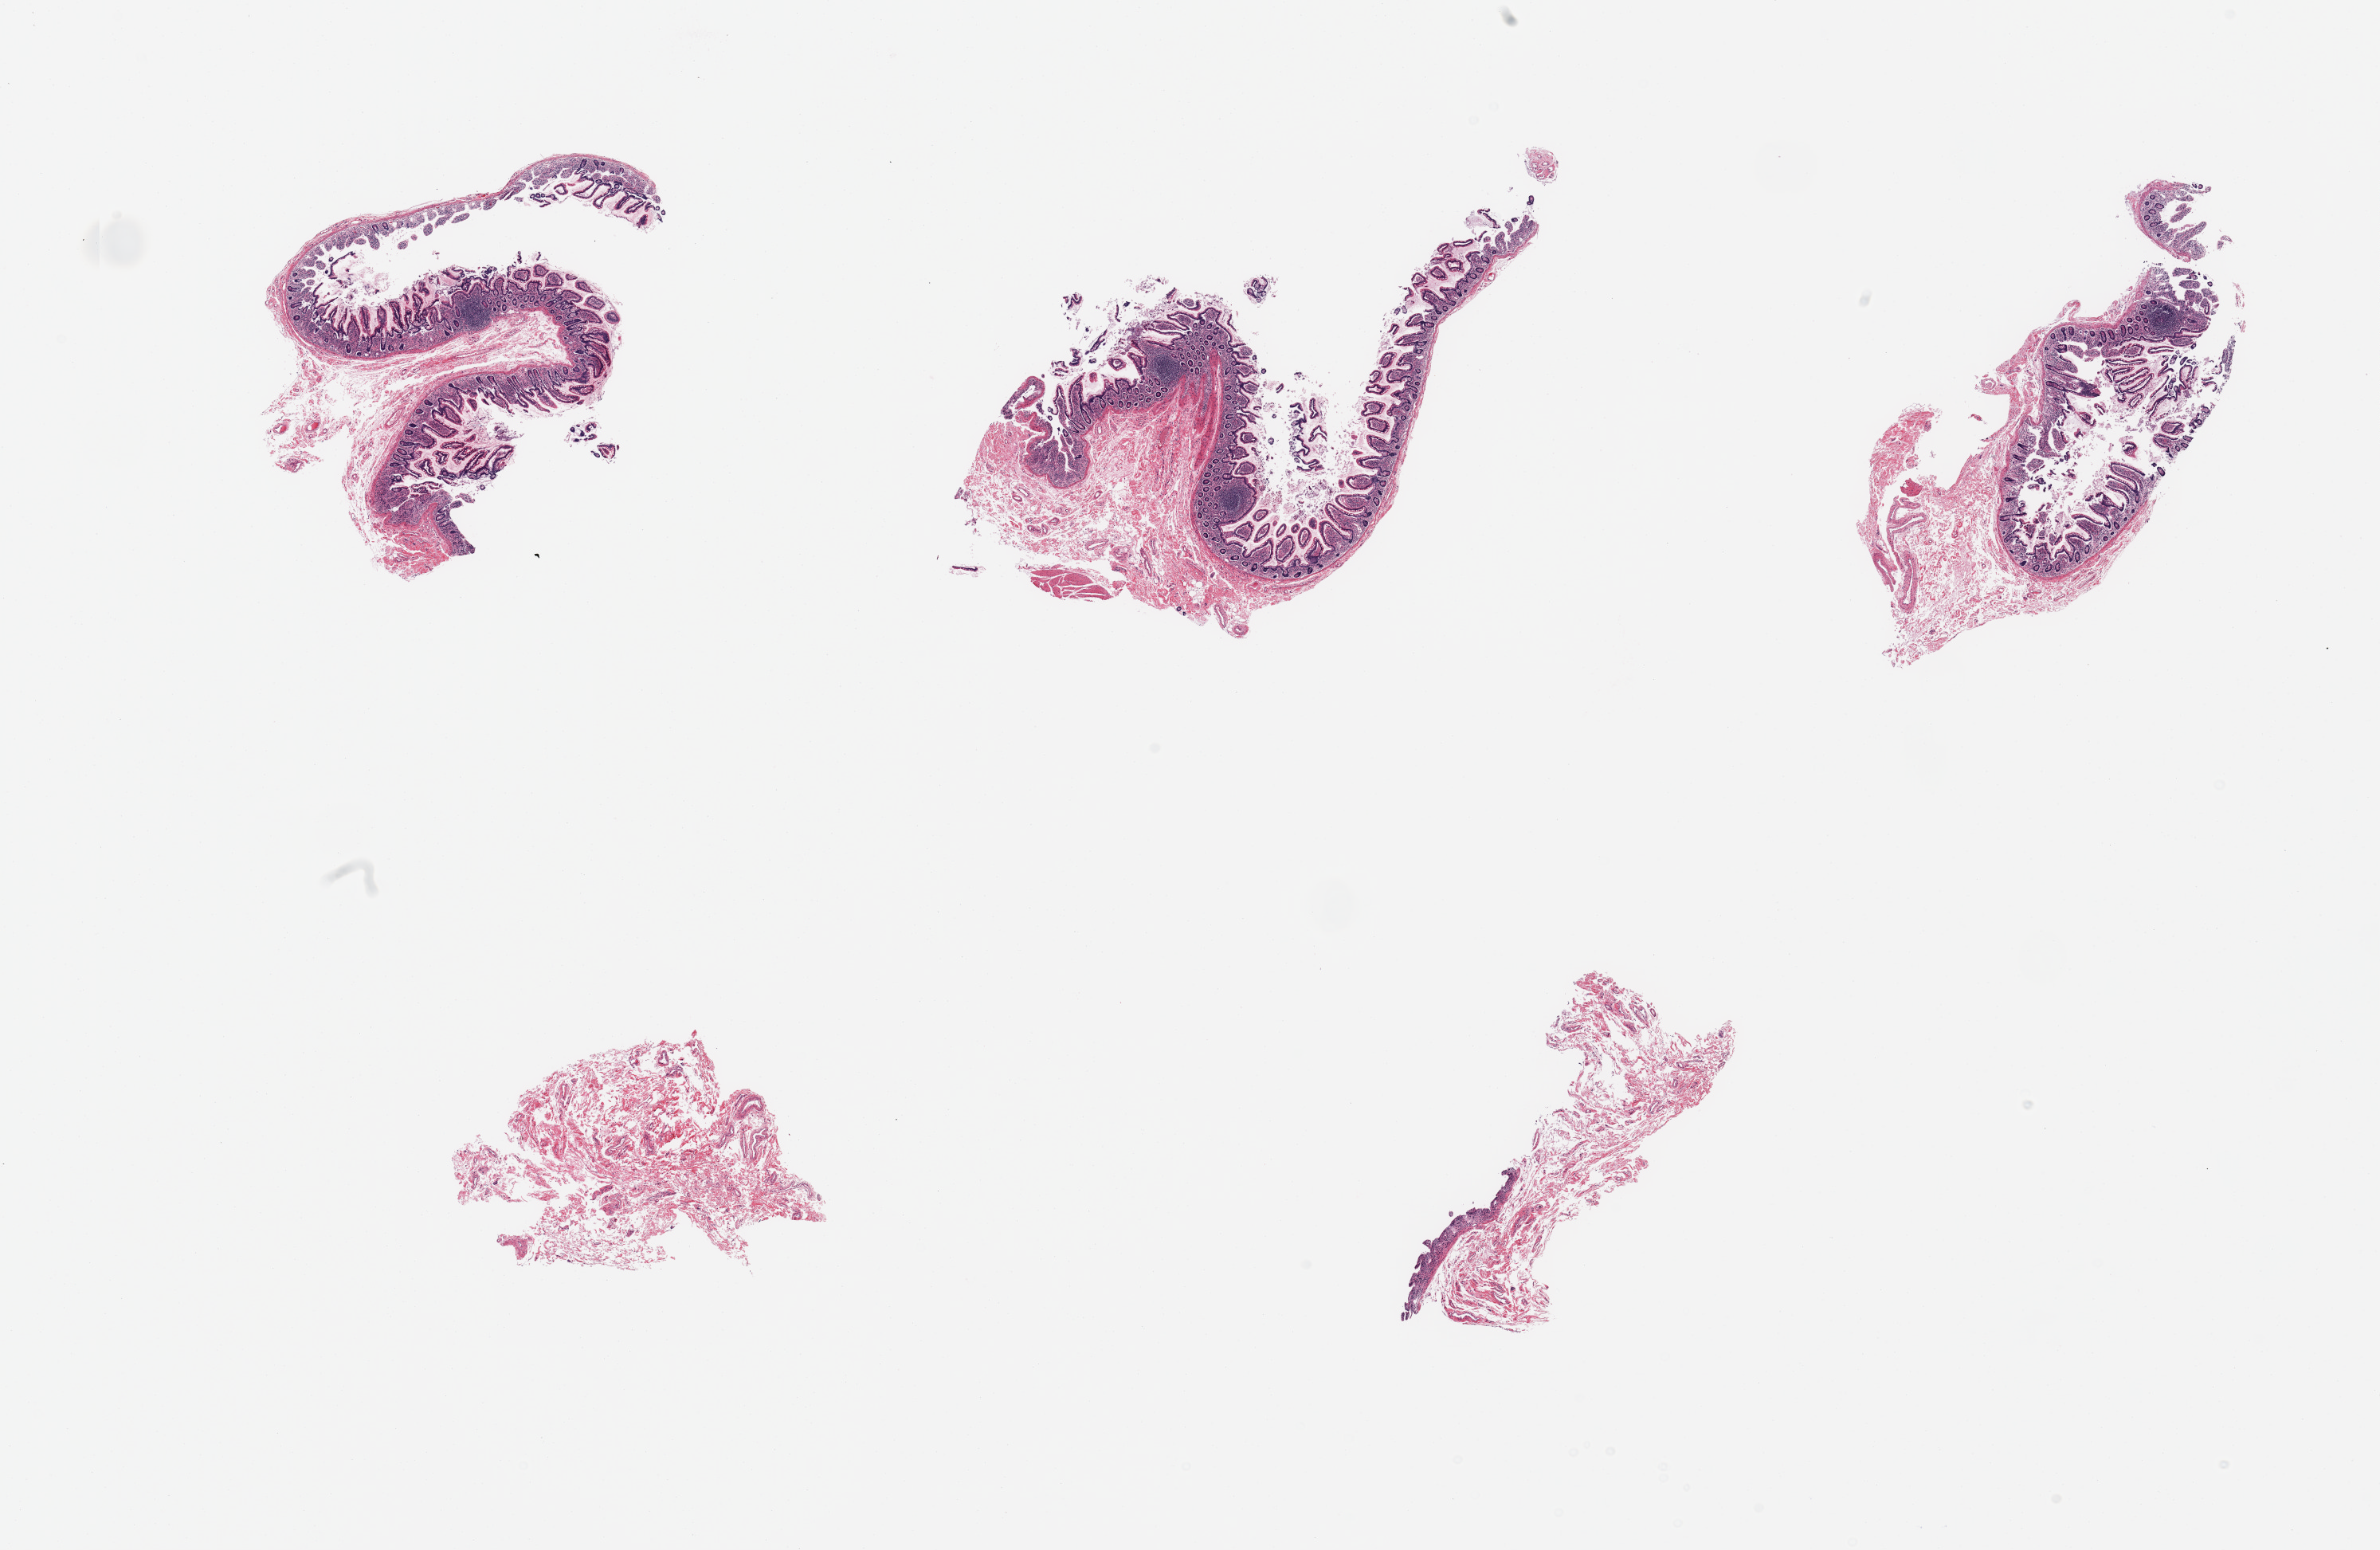
Whole-slide image, H&E stain, brightfield — whole scanned area (about 23.6 x 15.4 mm, from a 20x scan) shown as a low-resolution overview; PAXgene-fixed paraffin-embedded (PFPE) section; sampled site (target tissue): ileum; tissue donor sample. Donor: female.
• review note (as recorded): 5 pieces; predominantly mucosa with rare lymphoid follicle